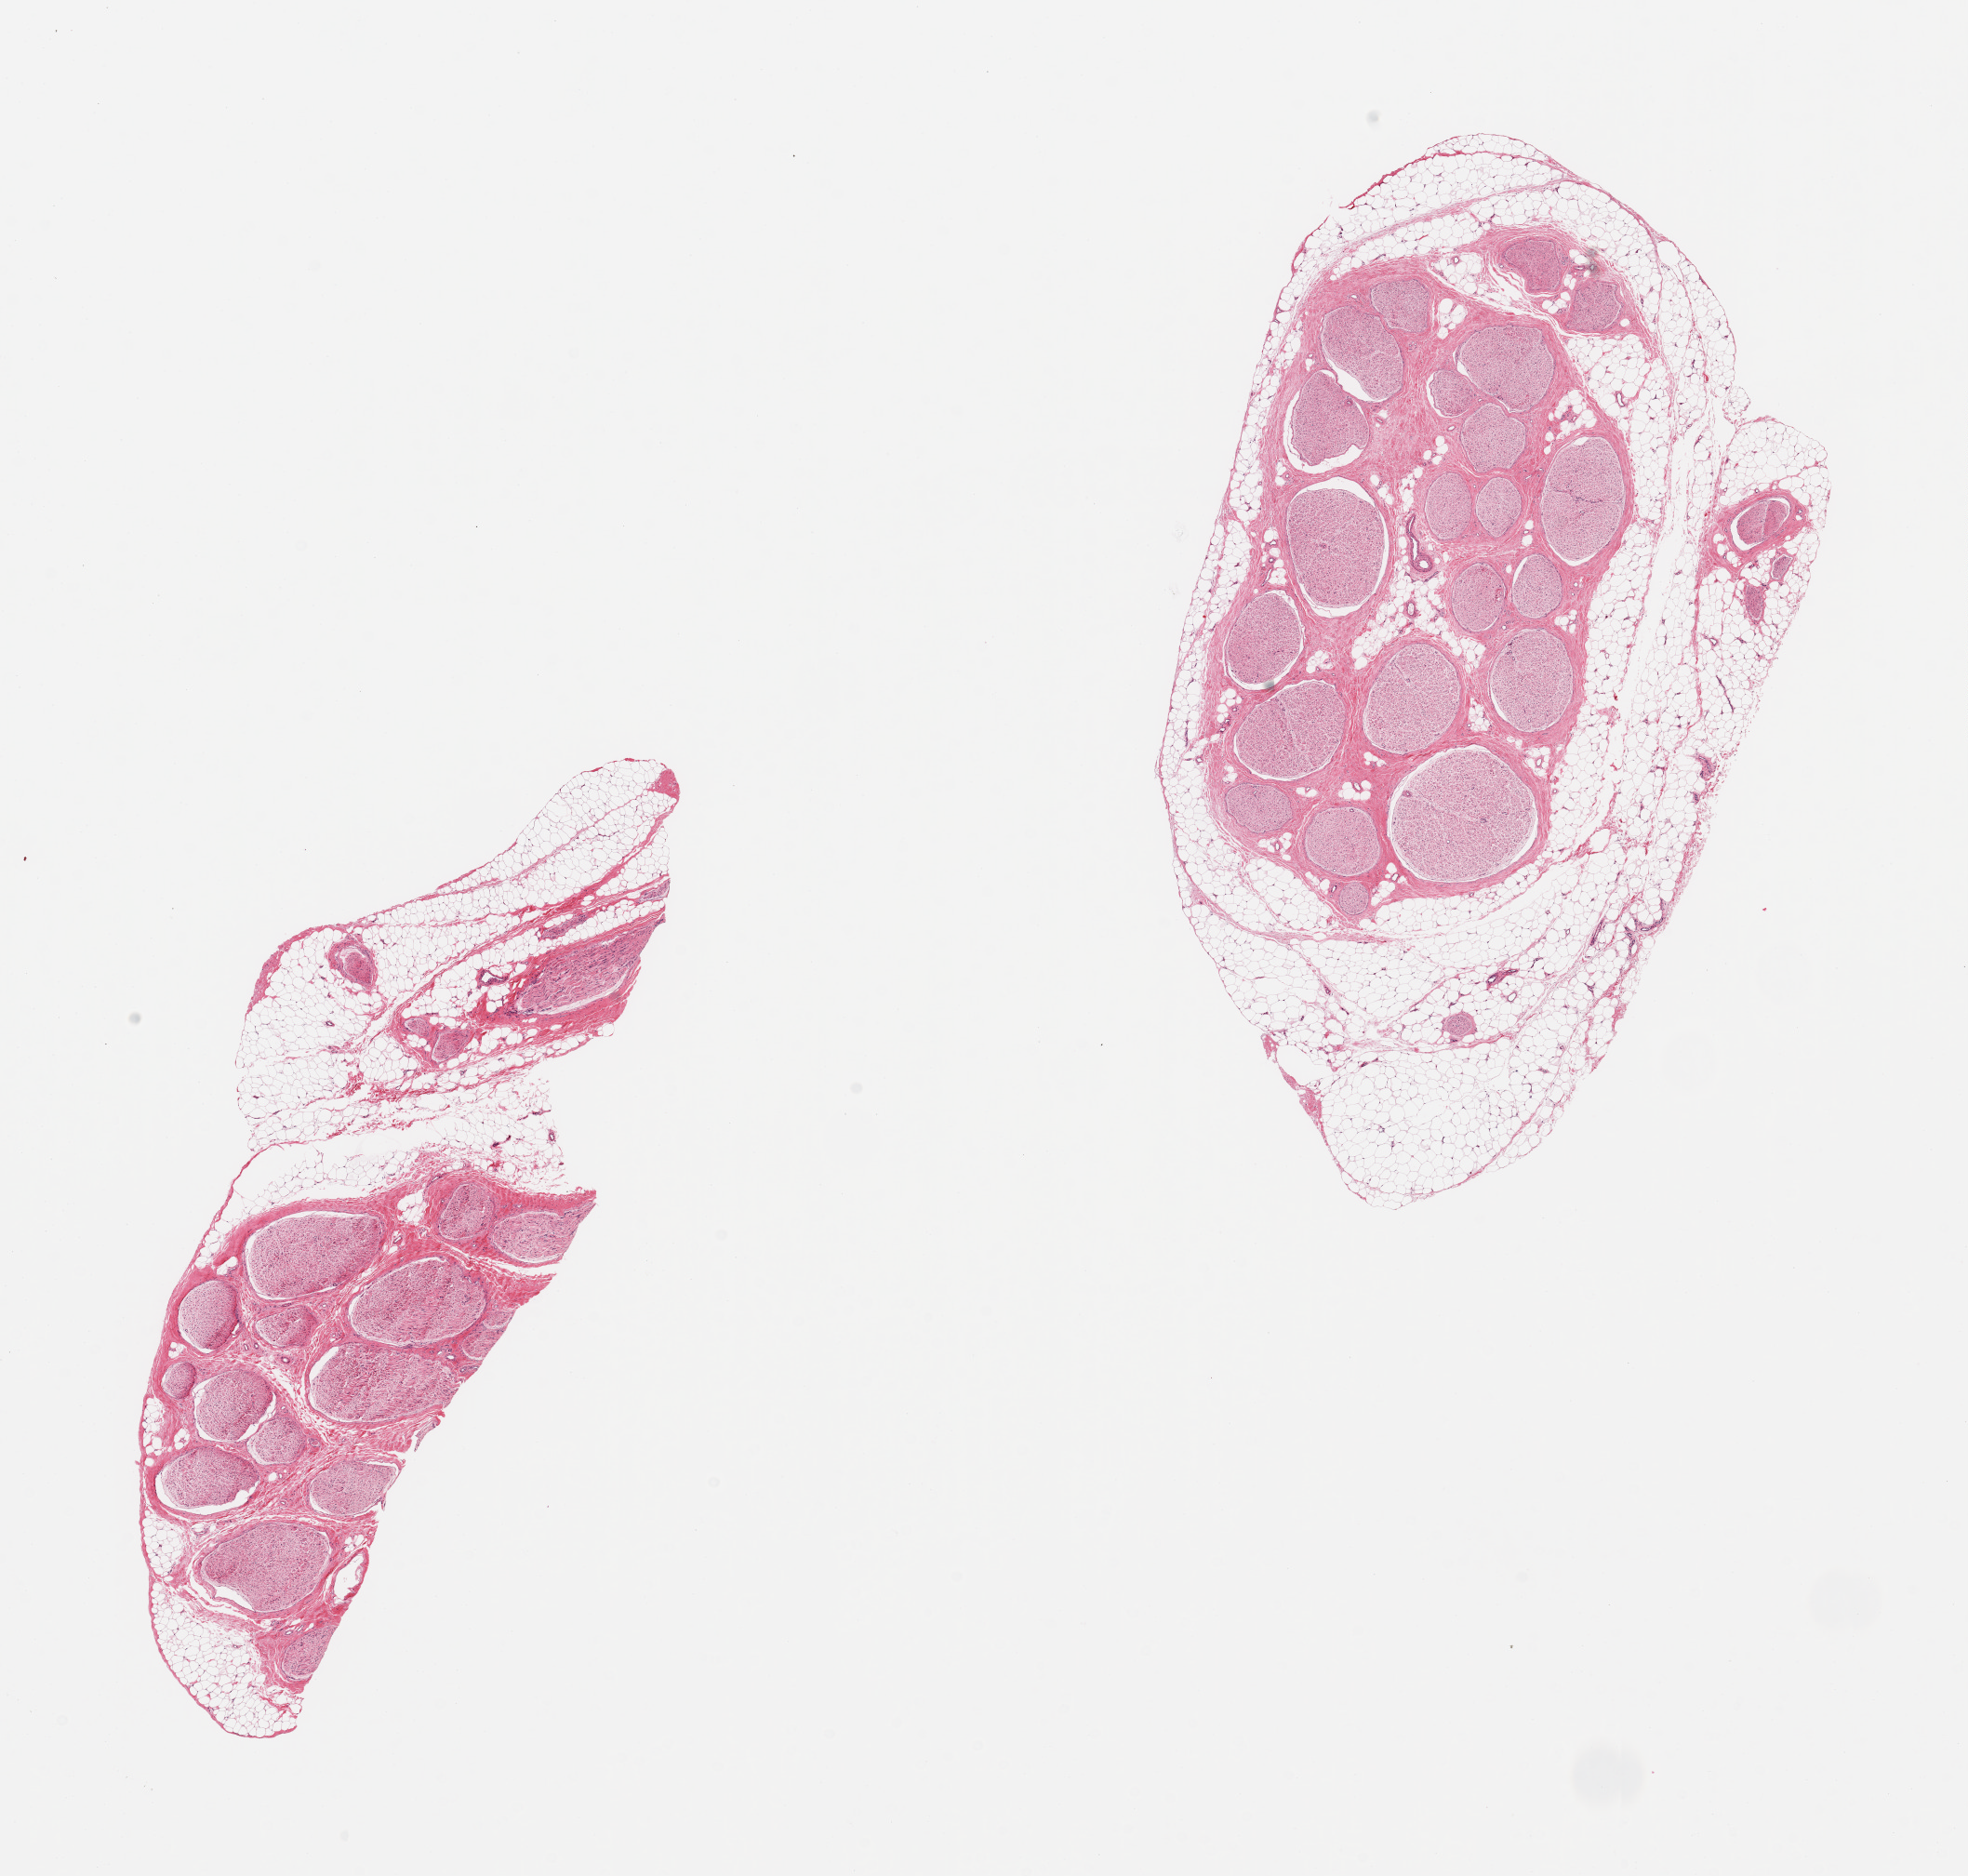
Whole-slide image, hematoxylin and eosin (H&E) stain — whole scanned area (about 16.7 x 16.0 mm, slide scanned at 20x) shown as a low-resolution overview. PAXgene-fixed, paraffin-embedded tissue. Target tissue: tibial nerve. Donor tissue sample. Donor: male.
Pathologist's review note for this sample: 2 pieces; include from 40-60% attached fat.